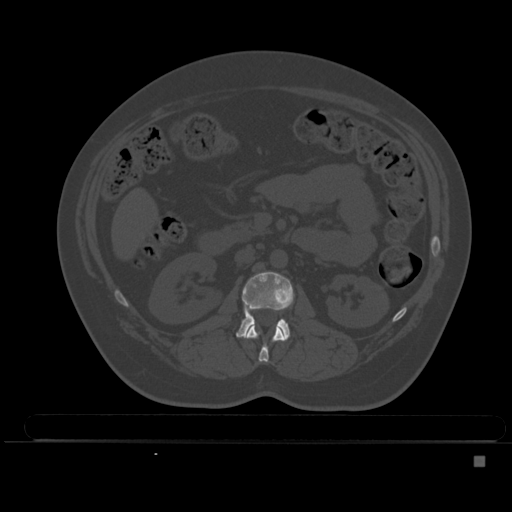
CT including the spine, one axial slice. Bone window (W 1800 / L 400 HU). 1.5 mm slice thickness. 512 × 512 image matrix, field of view 404 × 404 mm. Patient: female, 33 years. From the clinical record (not read from this slice): primary cancer: breast; vertebrae with lytic lesions (as recorded): T1.
Outlined on this slice (semi-automatically segmented with operator editing):
- L1 vertebra: box from (x=244, y=324) to (x=287, y=362) px
- L2 vertebra: (x=236, y=272)–(x=294, y=339)